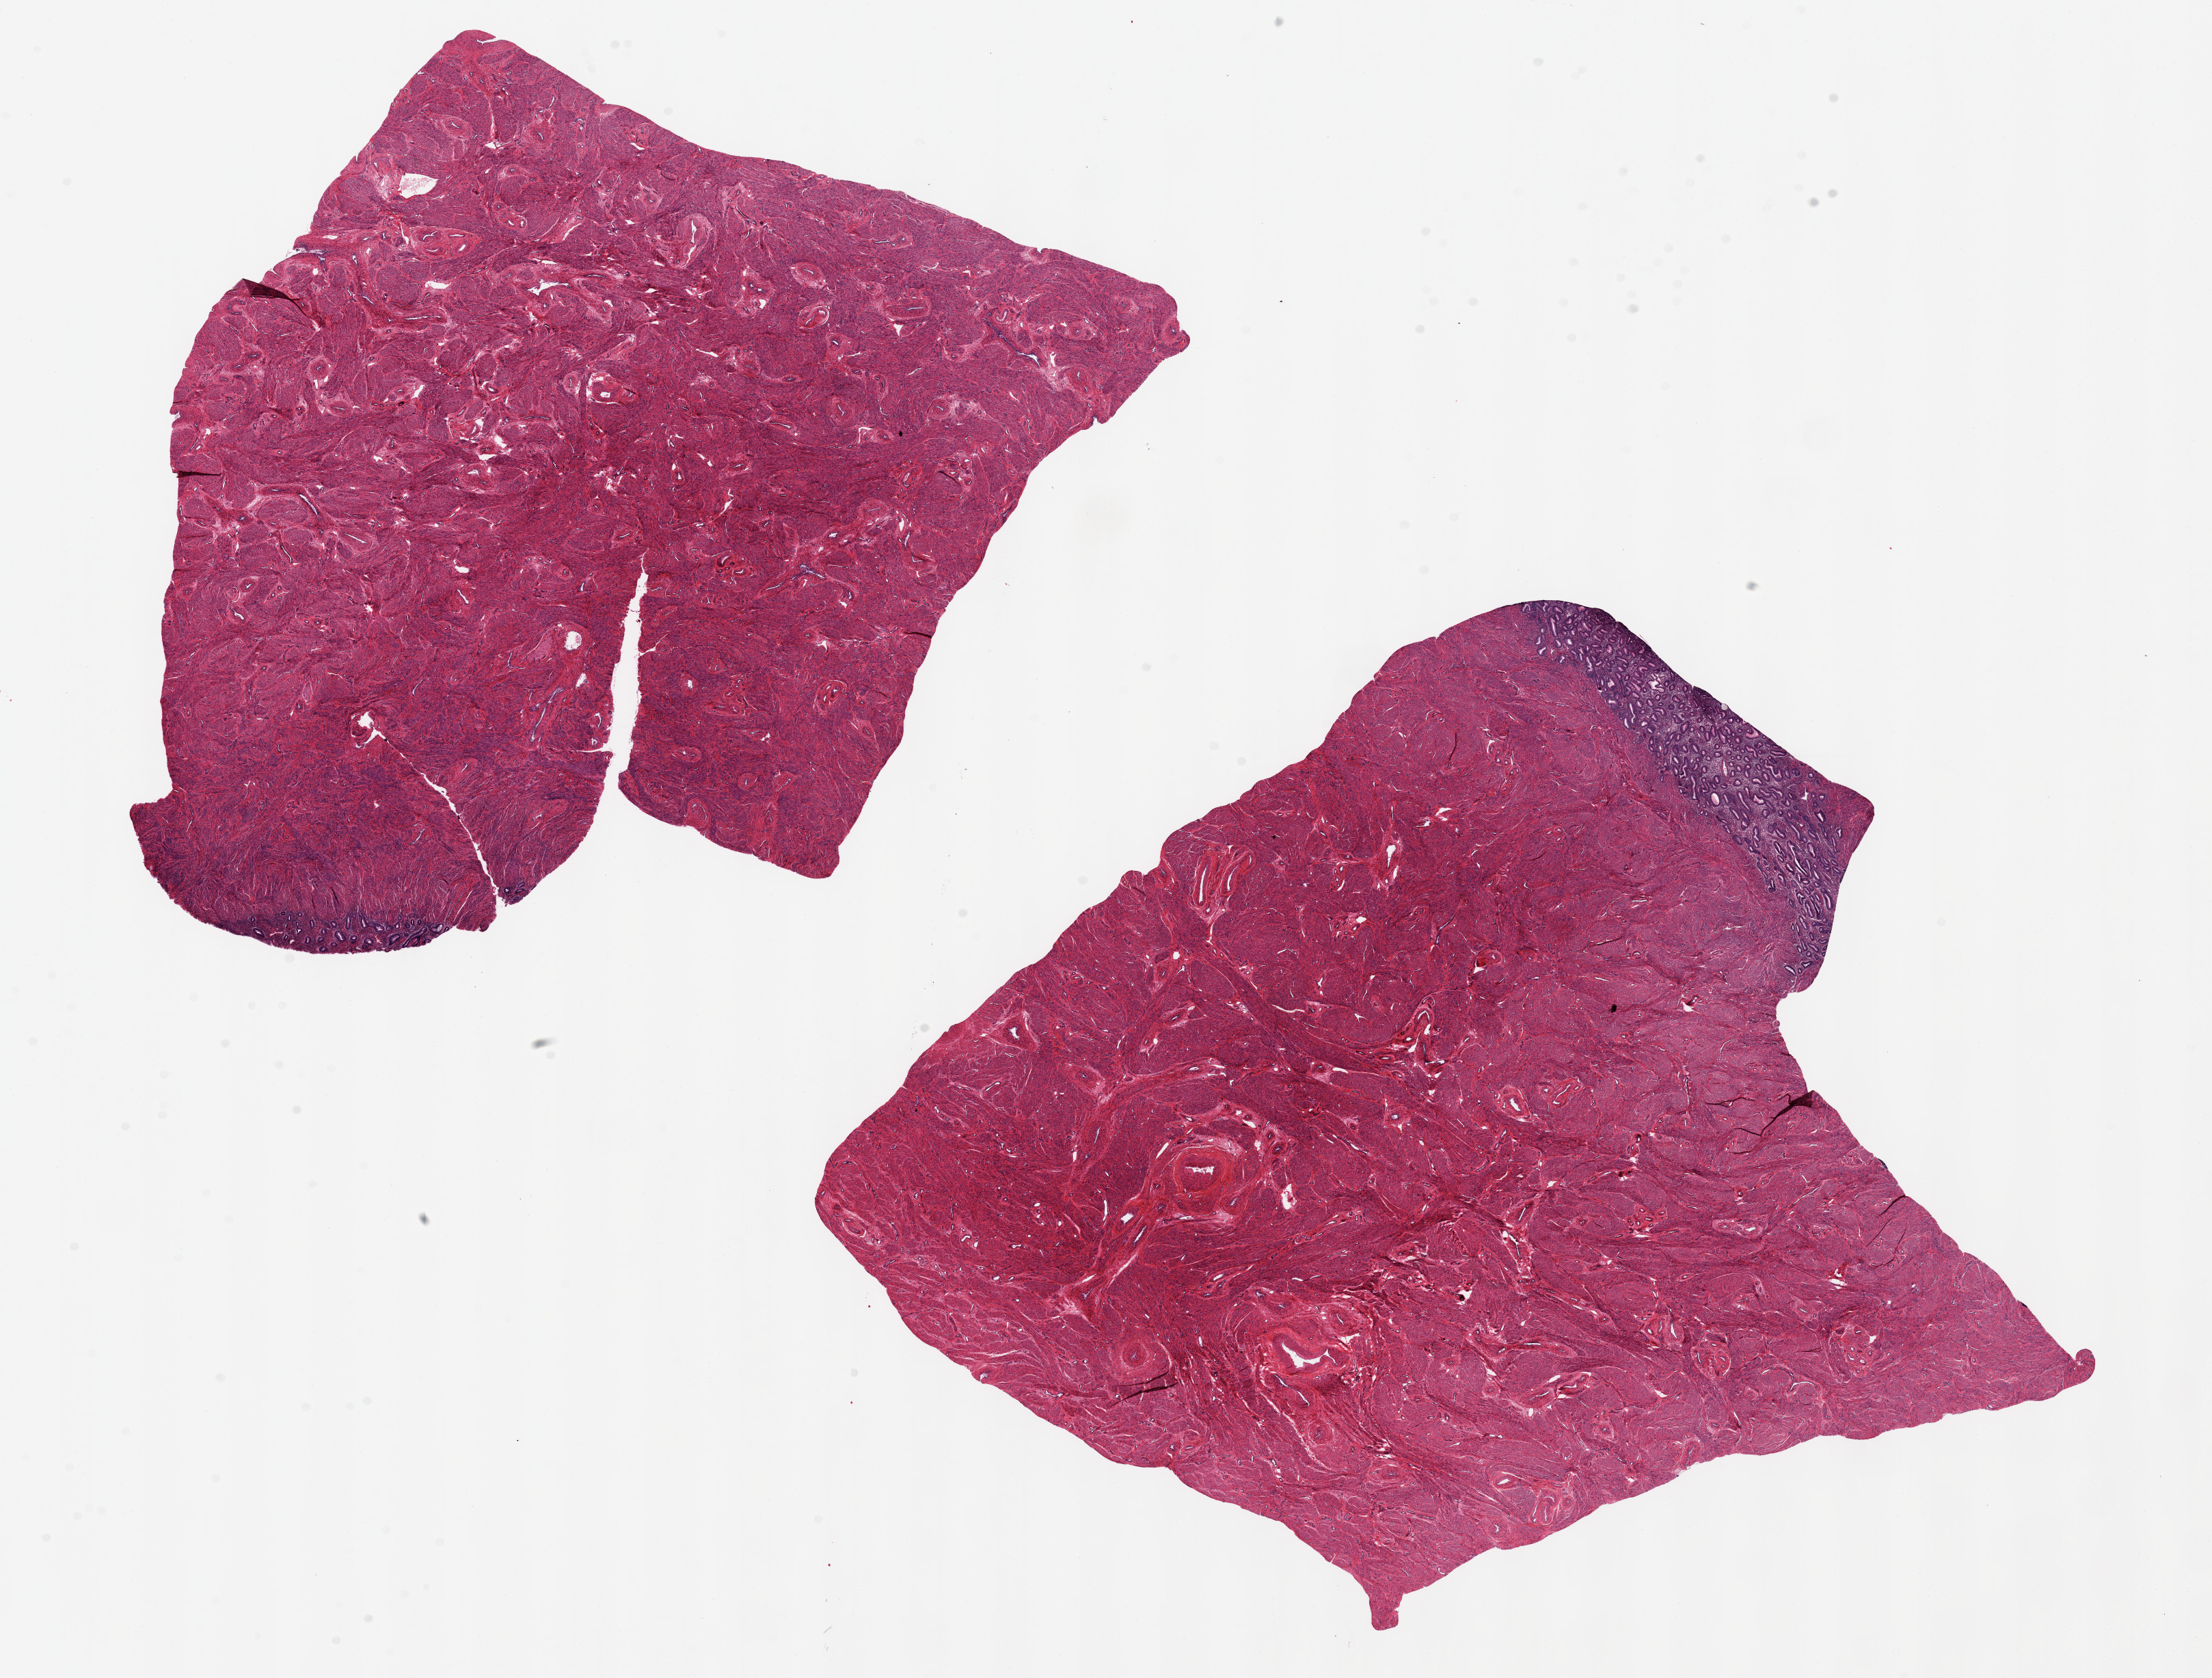
Hematoxylin and eosin (H&E) whole-slide image, brightfield — whole scanned area (about 25.6 x 19.4 mm, acquisition: 20x scan) shown as a low-resolution overview. PAXgene-fixed paraffin-embedded (PFPE) section. Target tissue: uterus. Tissue donor sample. Donor: female.
- pathologist's review note for this sample: 2 pieces, 10x9mm, 11x11mm; endometrium is 5x1 mm maximum